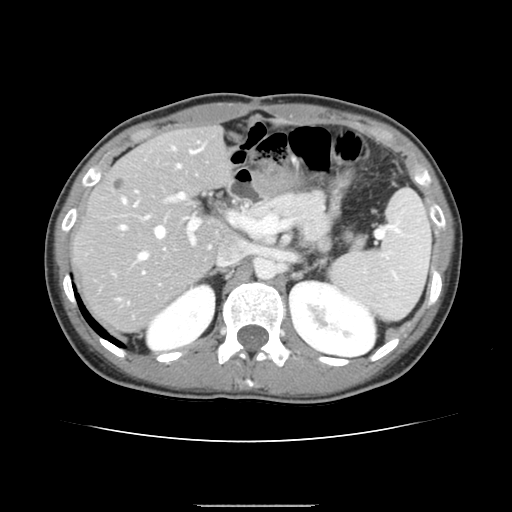
Contrast-enhanced abdominal CT, one axial slice. Slice 91 of 150 in the series (ordered by position). 120 kVp. Intravenous contrast given. Soft-tissue window (W 400 / L 40 HU). 512 × 512 image matrix. Female patient, age 32 years. Case-level facts recorded for this patient, not image findings: diagnosis: colorectal cancer liver metastases, imaged before liver resection; multiple liver metastases: yes; largest metastasis: 0.7 cm; disease in both lobes: no.
Annotated regions visible in this slice (outlined manually by an expert reader):
- hepatic veins: bounding box [x1, y1, x2, y2] px = [120, 149, 200, 259]
- liver: [74, 128, 230, 332]
- planned liver remnant (the part of the liver to remain after resection): [74, 128, 230, 277]
- portal vein (with intrahepatic branches): [118, 147, 234, 303]
- liver metastasis: [116, 180, 124, 191]